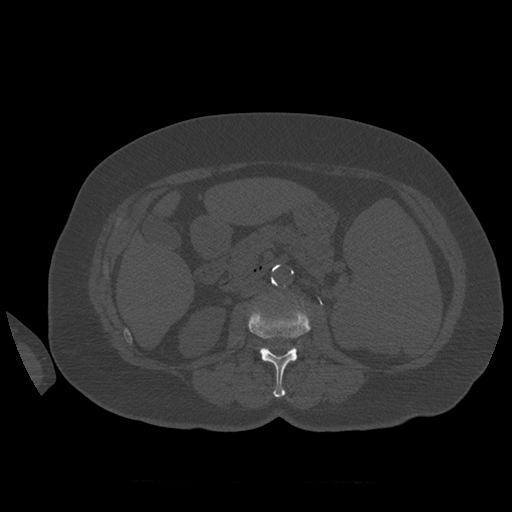
CT including the spine, one axial slice; position 249 of 399 along the scan axis; 120 kVp; bone window (W 1800 / L 400 HU); 1.25 mm slice thickness; 512 × 512 image matrix, field of view 404 × 404 mm. Patient age 81 years. From the clinical record (not read from this slice): primary cancer: renal; vertebrae with lytic lesions (as recorded): L1.
Structures marked on this image (semi-automatic segmentation, software-assisted and operator-edited):
- L2 vertebra: bounding box (x1, y1, x2, y2) in pixels: (249, 305, 311, 398)